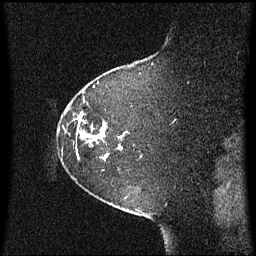
Breast MRI (dynamic contrast-enhanced), one sagittal slice; slice 53 of 60 in the series (ordered by position); dynamic contrast-enhanced series, image 2 of 3 at this slice position (ordered by acquisition); 1.5 T; TE 4.2 ms, TR 8.4 ms; 2 mm slice thickness; 256 × 256 image matrix. Patient: female, 60 years. From the clinical record (not read from this slice): setting: breast cancer imaged before/during neoadjuvant chemotherapy; receptor status: triple-negative.
Outlined on this slice (semi-automatic segmentation, software-assisted and operator-edited):
- analysis volume of interest (the breast-tissue region the enhancement analysis was run in; not a lesion): bounding box [x1, y1, x2, y2] px = [59, 109, 130, 161]
- tumour enhancement mask (voxels above the 70 % enhancement threshold inside the analysis volume of interest): [84, 132, 105, 139]